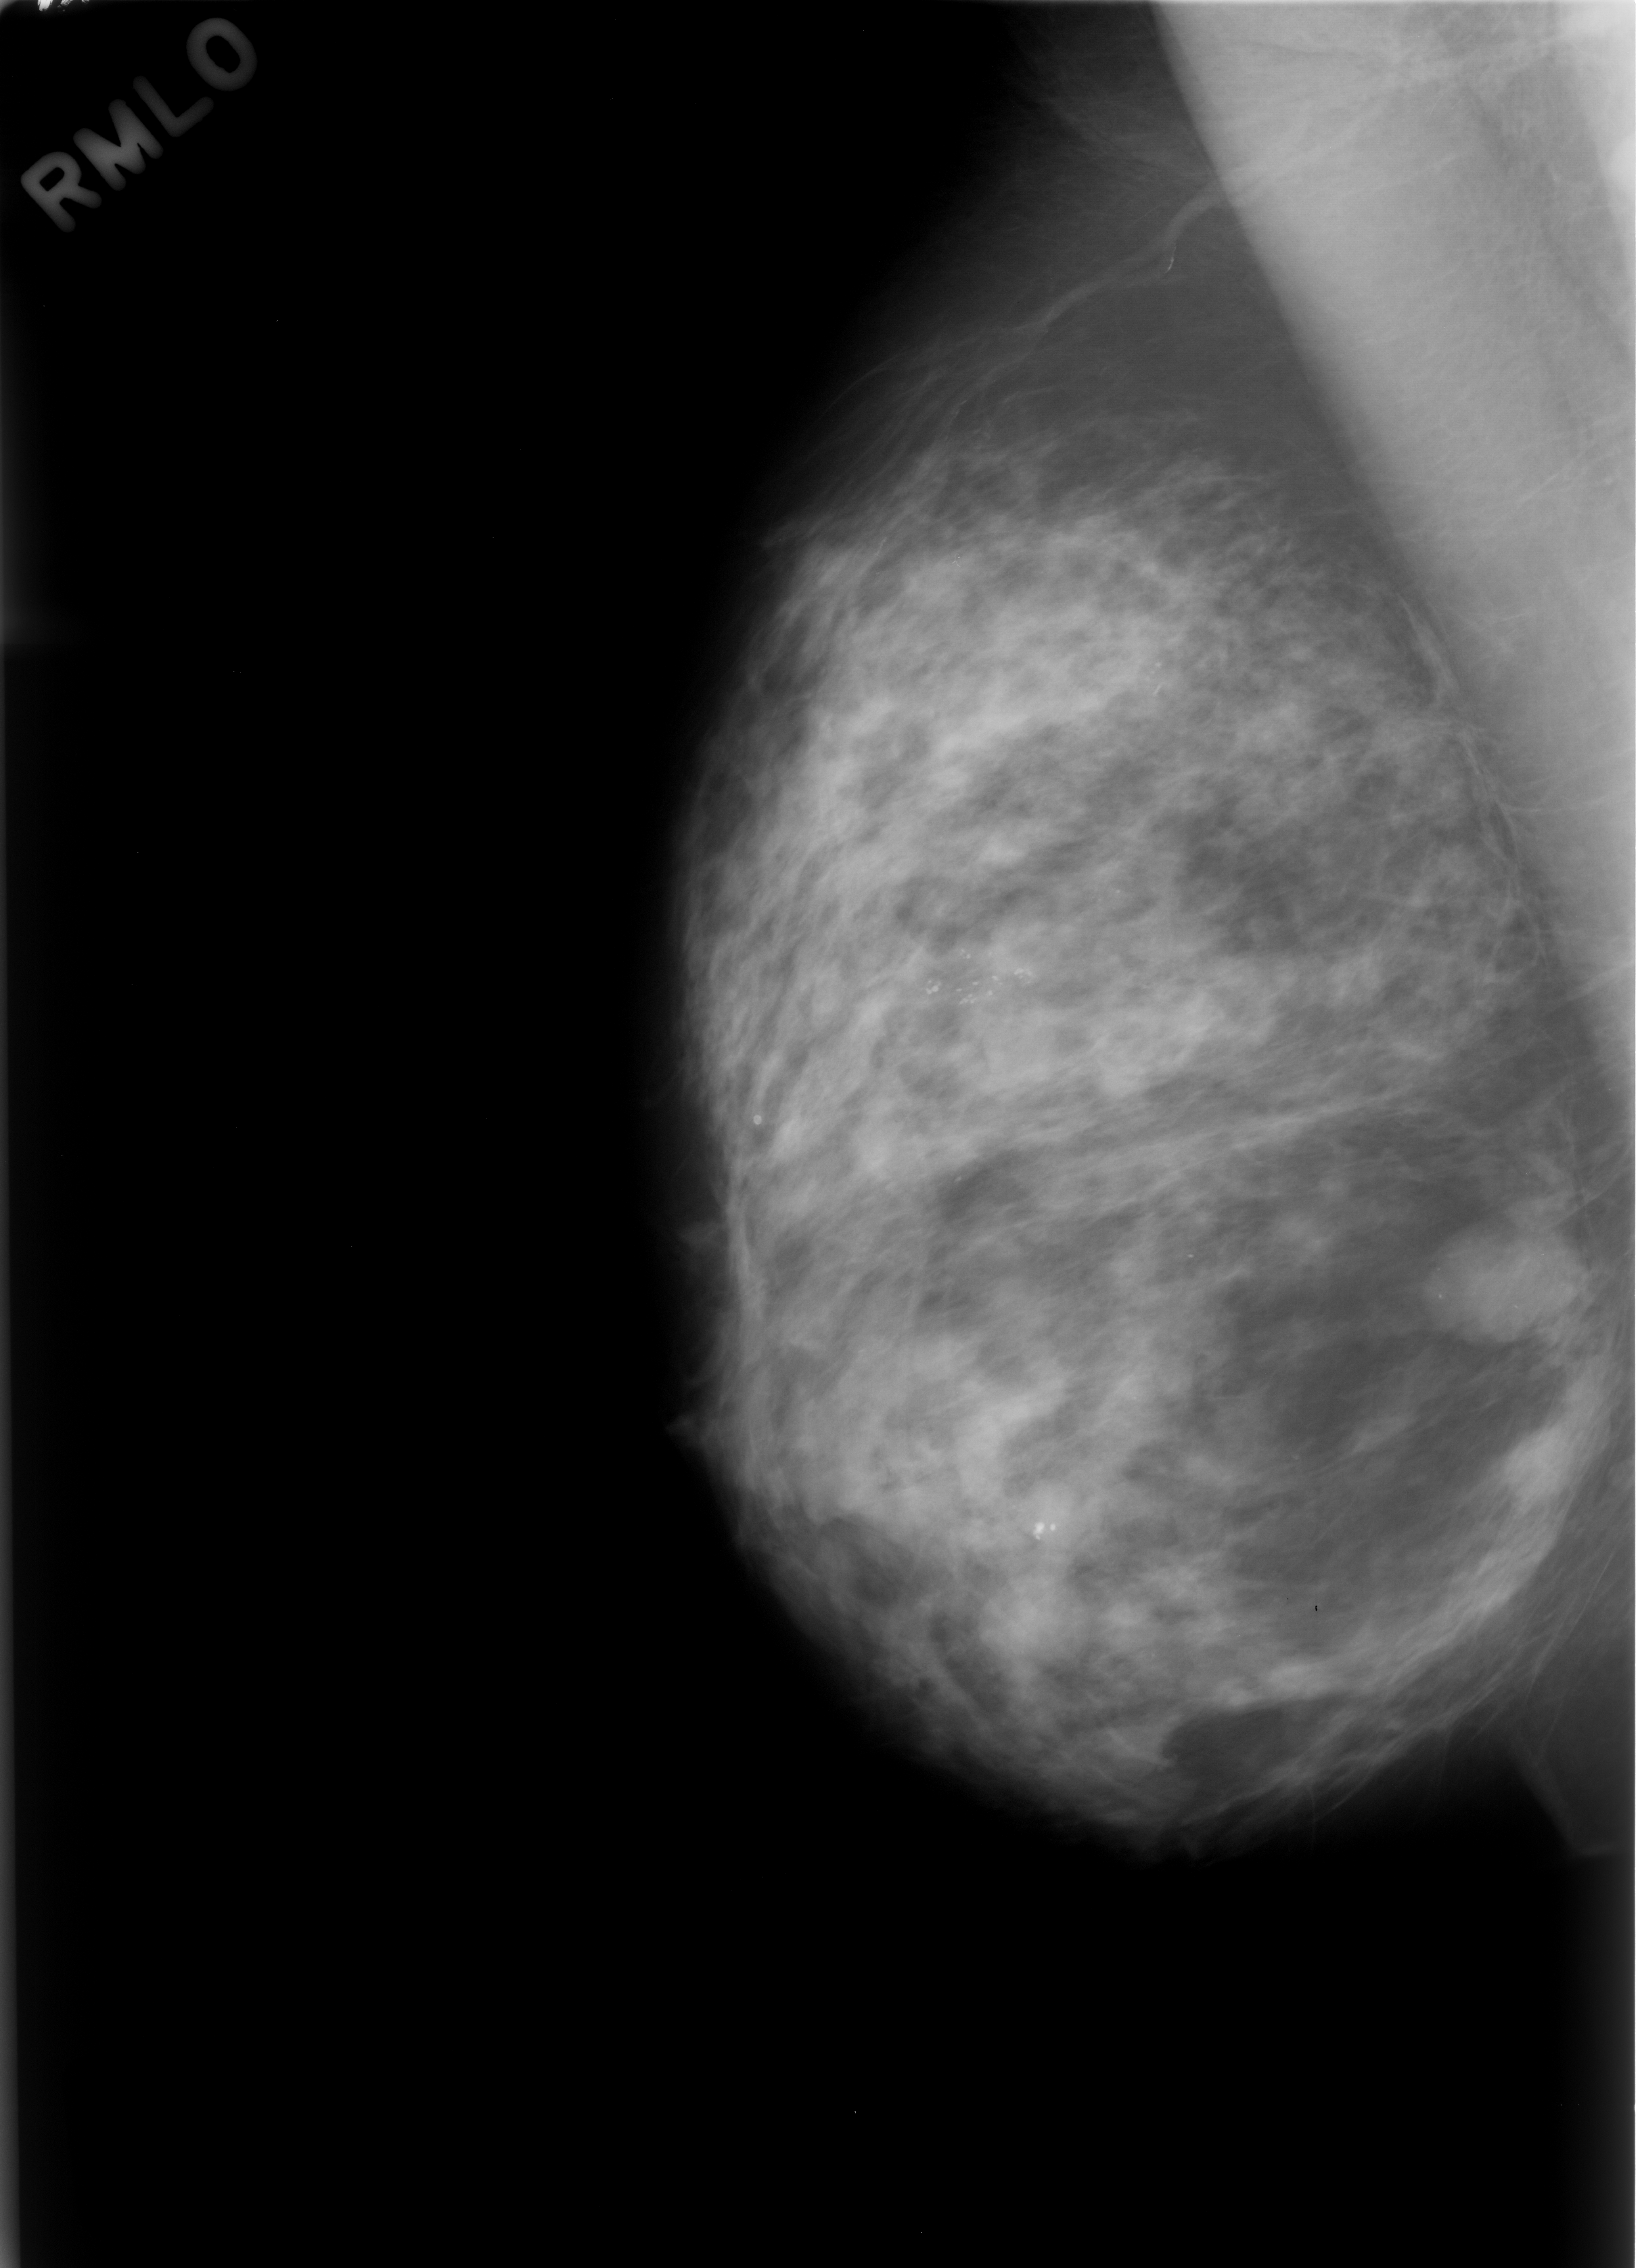
Scanned film-screen mammogram, right breast, MLO view, BI-RADS breast density category 3 (scale 1–4).
Abnormality record for this image: mass, shape lobulated, margins circumscribed; BI-RADS assessment category 3; pathology result (as recorded, not read from the image): benign.